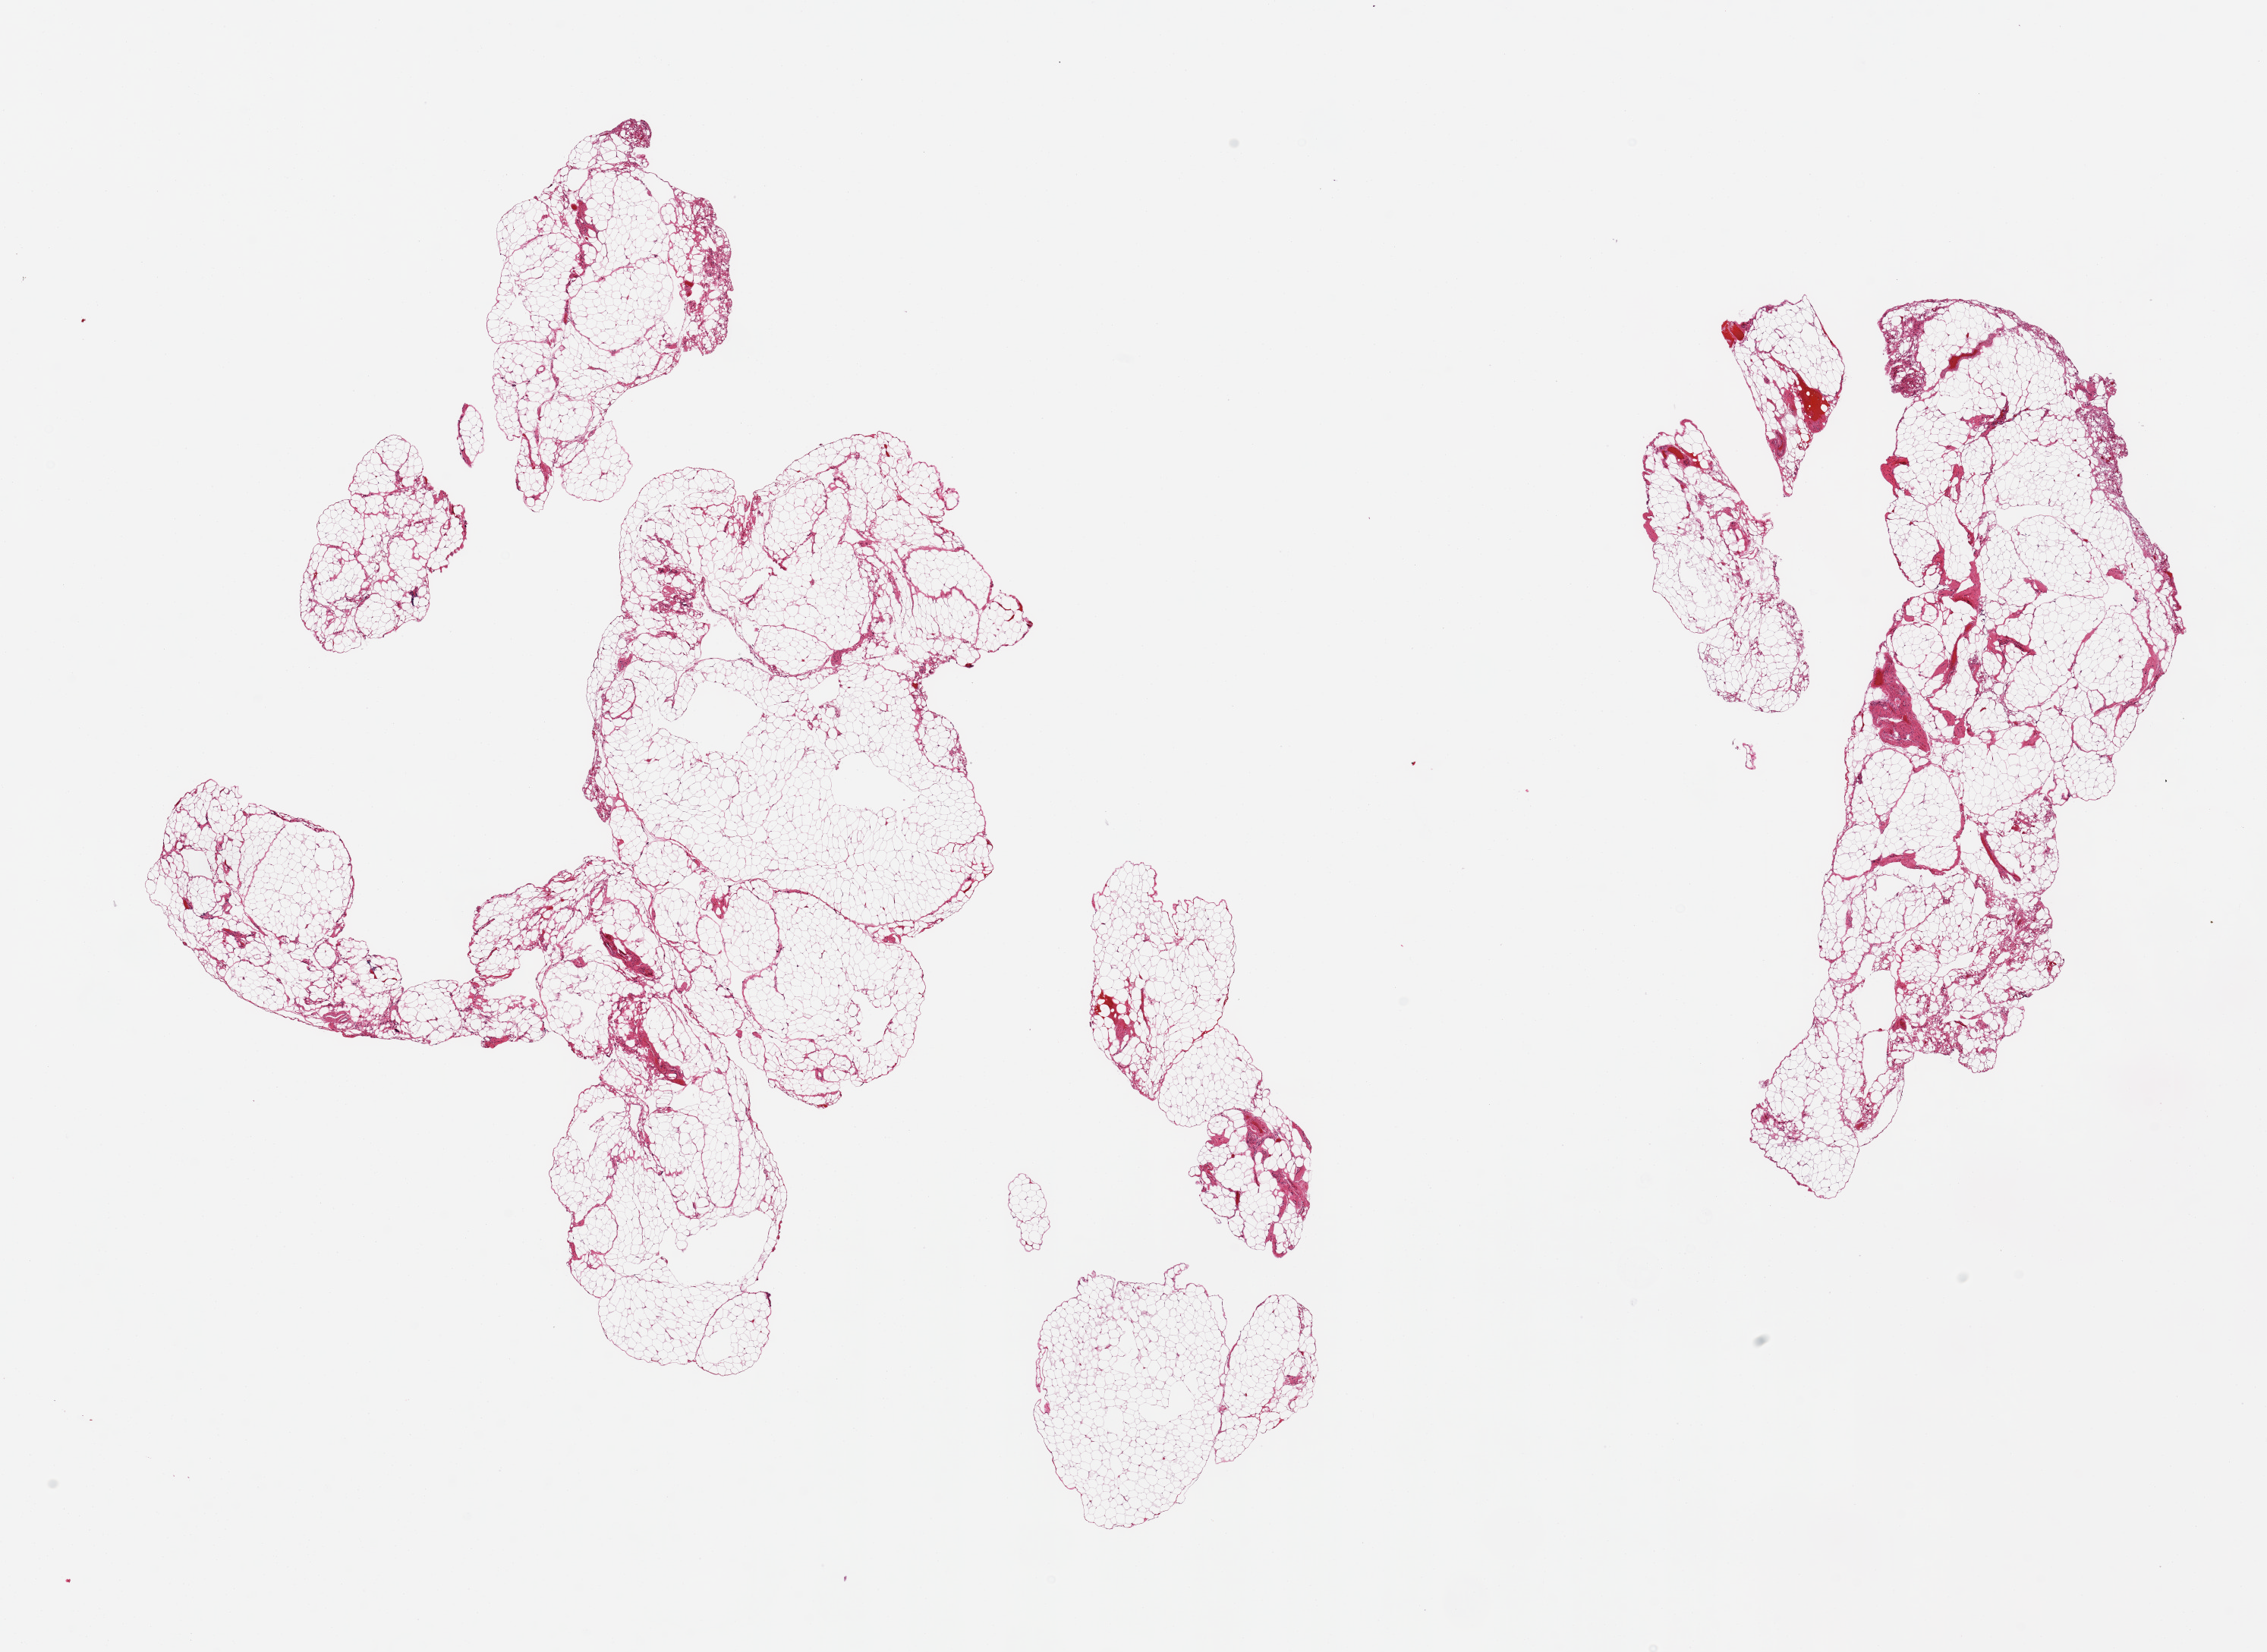
Hematoxylin and eosin (H&E) whole-slide image — low-resolution overview of the scanned area, about 23.6 x 17.2 mm (slide scanned at 20x), PAXgene-fixed, paraffin-embedded tissue, target tissue: omentum, donor tissue sample. Donor: male.
Review note (as recorded): 2 pieces, ~5-10% fascia/vascular elements.